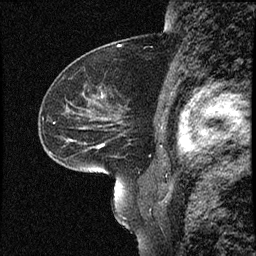
Breast MRI (dynamic contrast-enhanced), one sagittal slice; dynamic contrast-enhanced study with each time point stored as its own series, time point 2 of 4 at this slice position (early post-contrast, ordered by acquisition time); 1.5 T; TE 4.2 ms, TR 16.7 ms; 2 mm slice thickness; 256 × 256 image matrix, field of view 200 × 200 mm. Patient: female, 52 years. From the clinical record (not read from this slice): setting: breast cancer imaged before/during neoadjuvant chemotherapy; receptor status: HER2-positive.
Outlined on this slice (semi-automatic segmentation, software-assisted and operator-edited):
- analysis volume of interest (the breast-tissue region the enhancement analysis was run in; not a lesion): bounding box (x1, y1, x2, y2) in pixels: (38, 79, 165, 181)
- tumour enhancement mask (voxels above the 100 % enhancement threshold inside the analysis volume of interest): (99, 145, 102, 148)